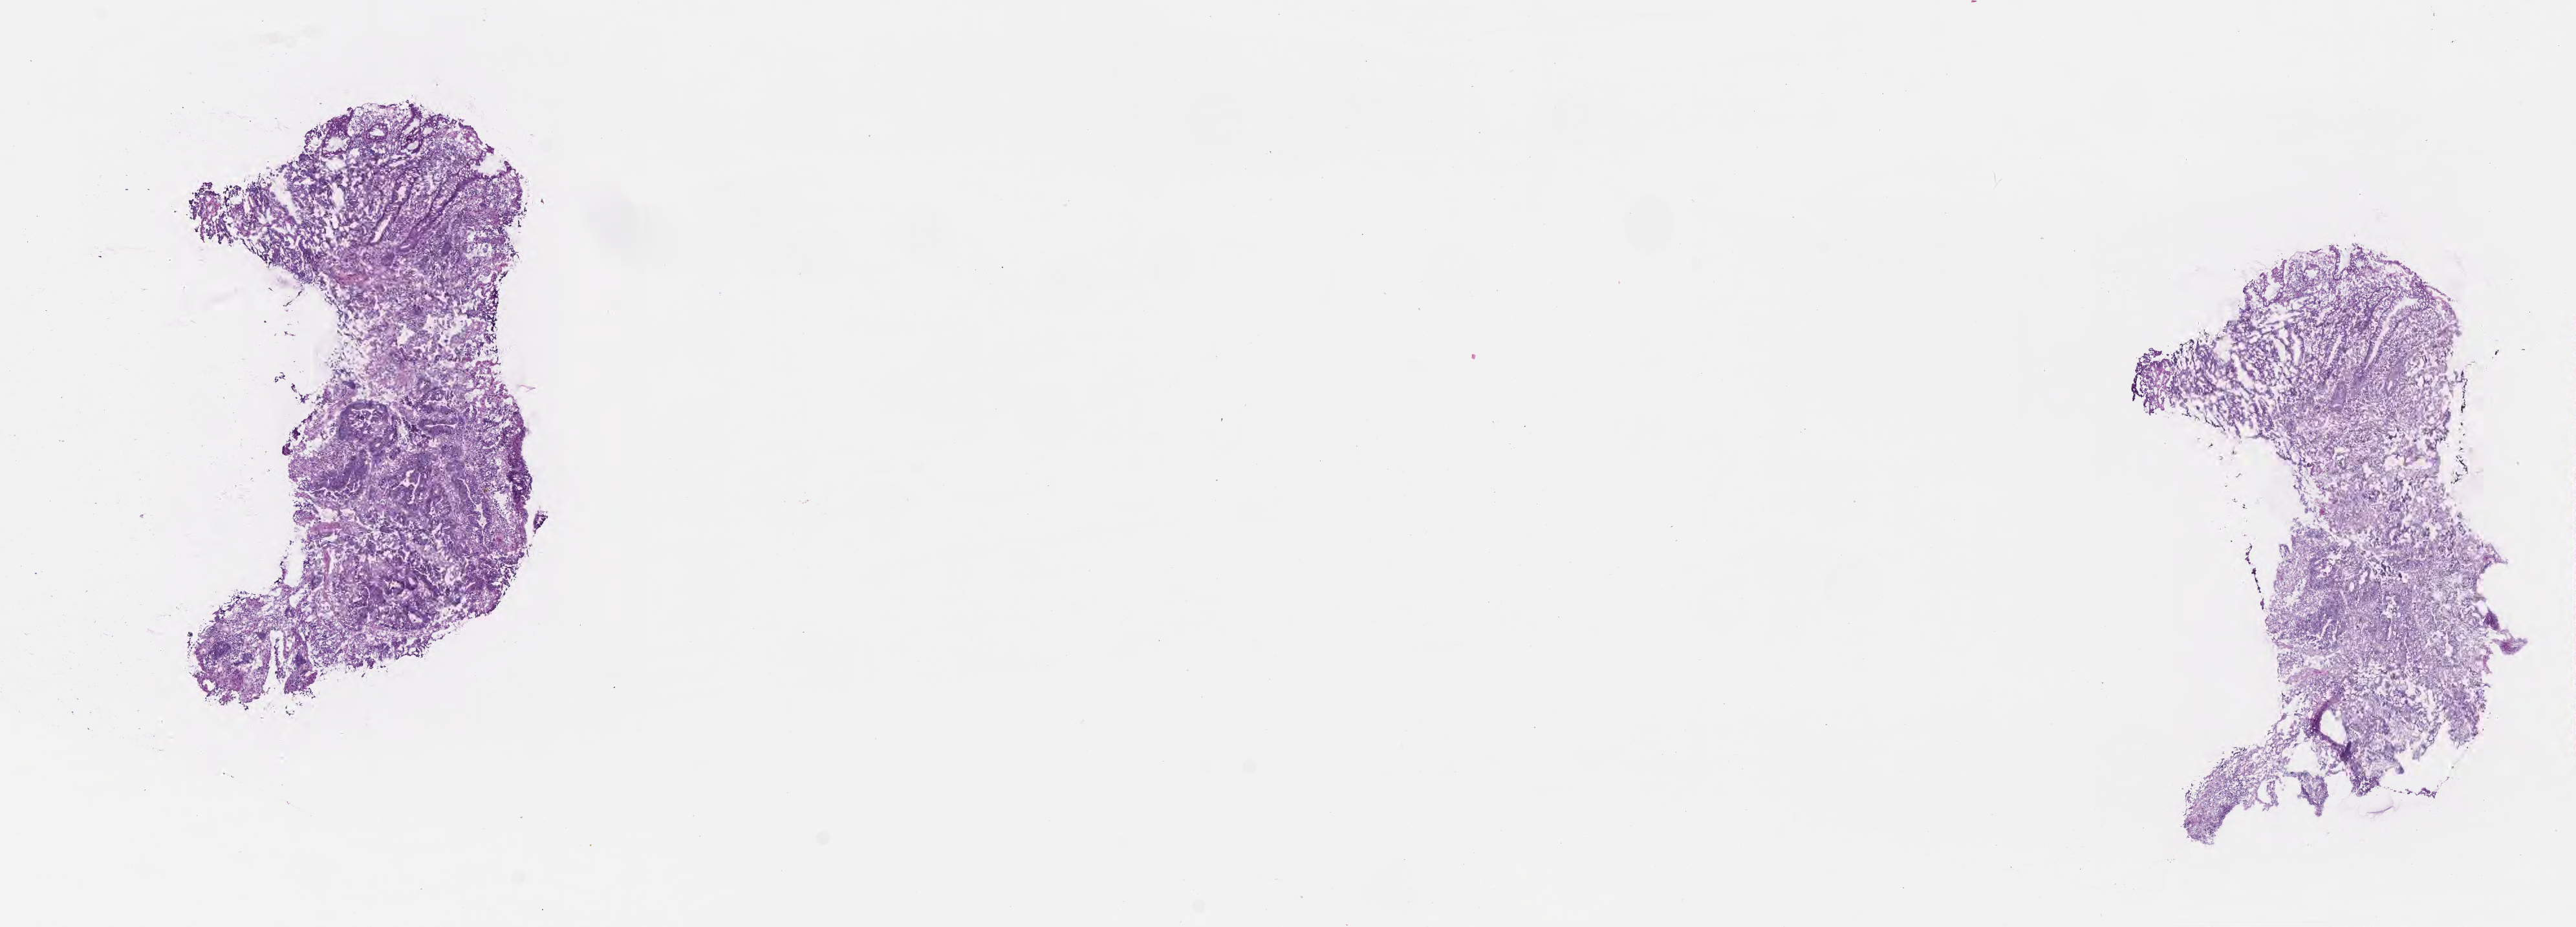
H&E whole-slide image — whole scanned area (about 16.1 x 5.8 mm) shown as a low-resolution overview; cryosection; primary tumor; anatomic site: sigmoid colon. Male, age 75 years at initial diagnosis. Tumor grade: G2 (moderately differentiated). Pathologist review of this section (percent, as recorded): tumor cells 80%, tumor nuclei 80%, stromal cells 18%, necrosis 0%, normal cells 2%. Infiltration values recorded for this section: lymphocyte infiltration 5%, monocyte infiltration 2%, neutrophil infiltration 7%.
• AJCC pathologic stage: Stage IIA
• diagnosis: Adenocarcinoma, NOS